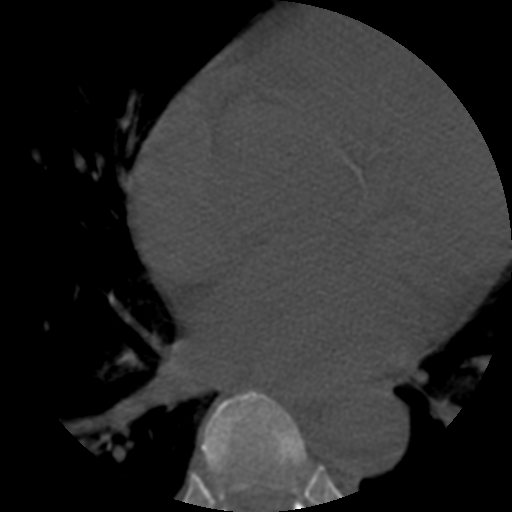
CT including the spine, one axial slice; position 344 of 508 along the scan axis; 120 kVp; bone window (W 1800 / L 400 HU); 512 × 512 image matrix, field of view 160 × 160 mm. Patient age 57 years. From the clinical record (not read from this slice): primary cancer: prostate.
Outlined on this slice (semi-automatically segmented with operator editing):
- T6 vertebra: bounding box [x1, y1, x2, y2] px = [201, 390, 309, 508]
- T7 vertebra: [292, 487, 304, 512]